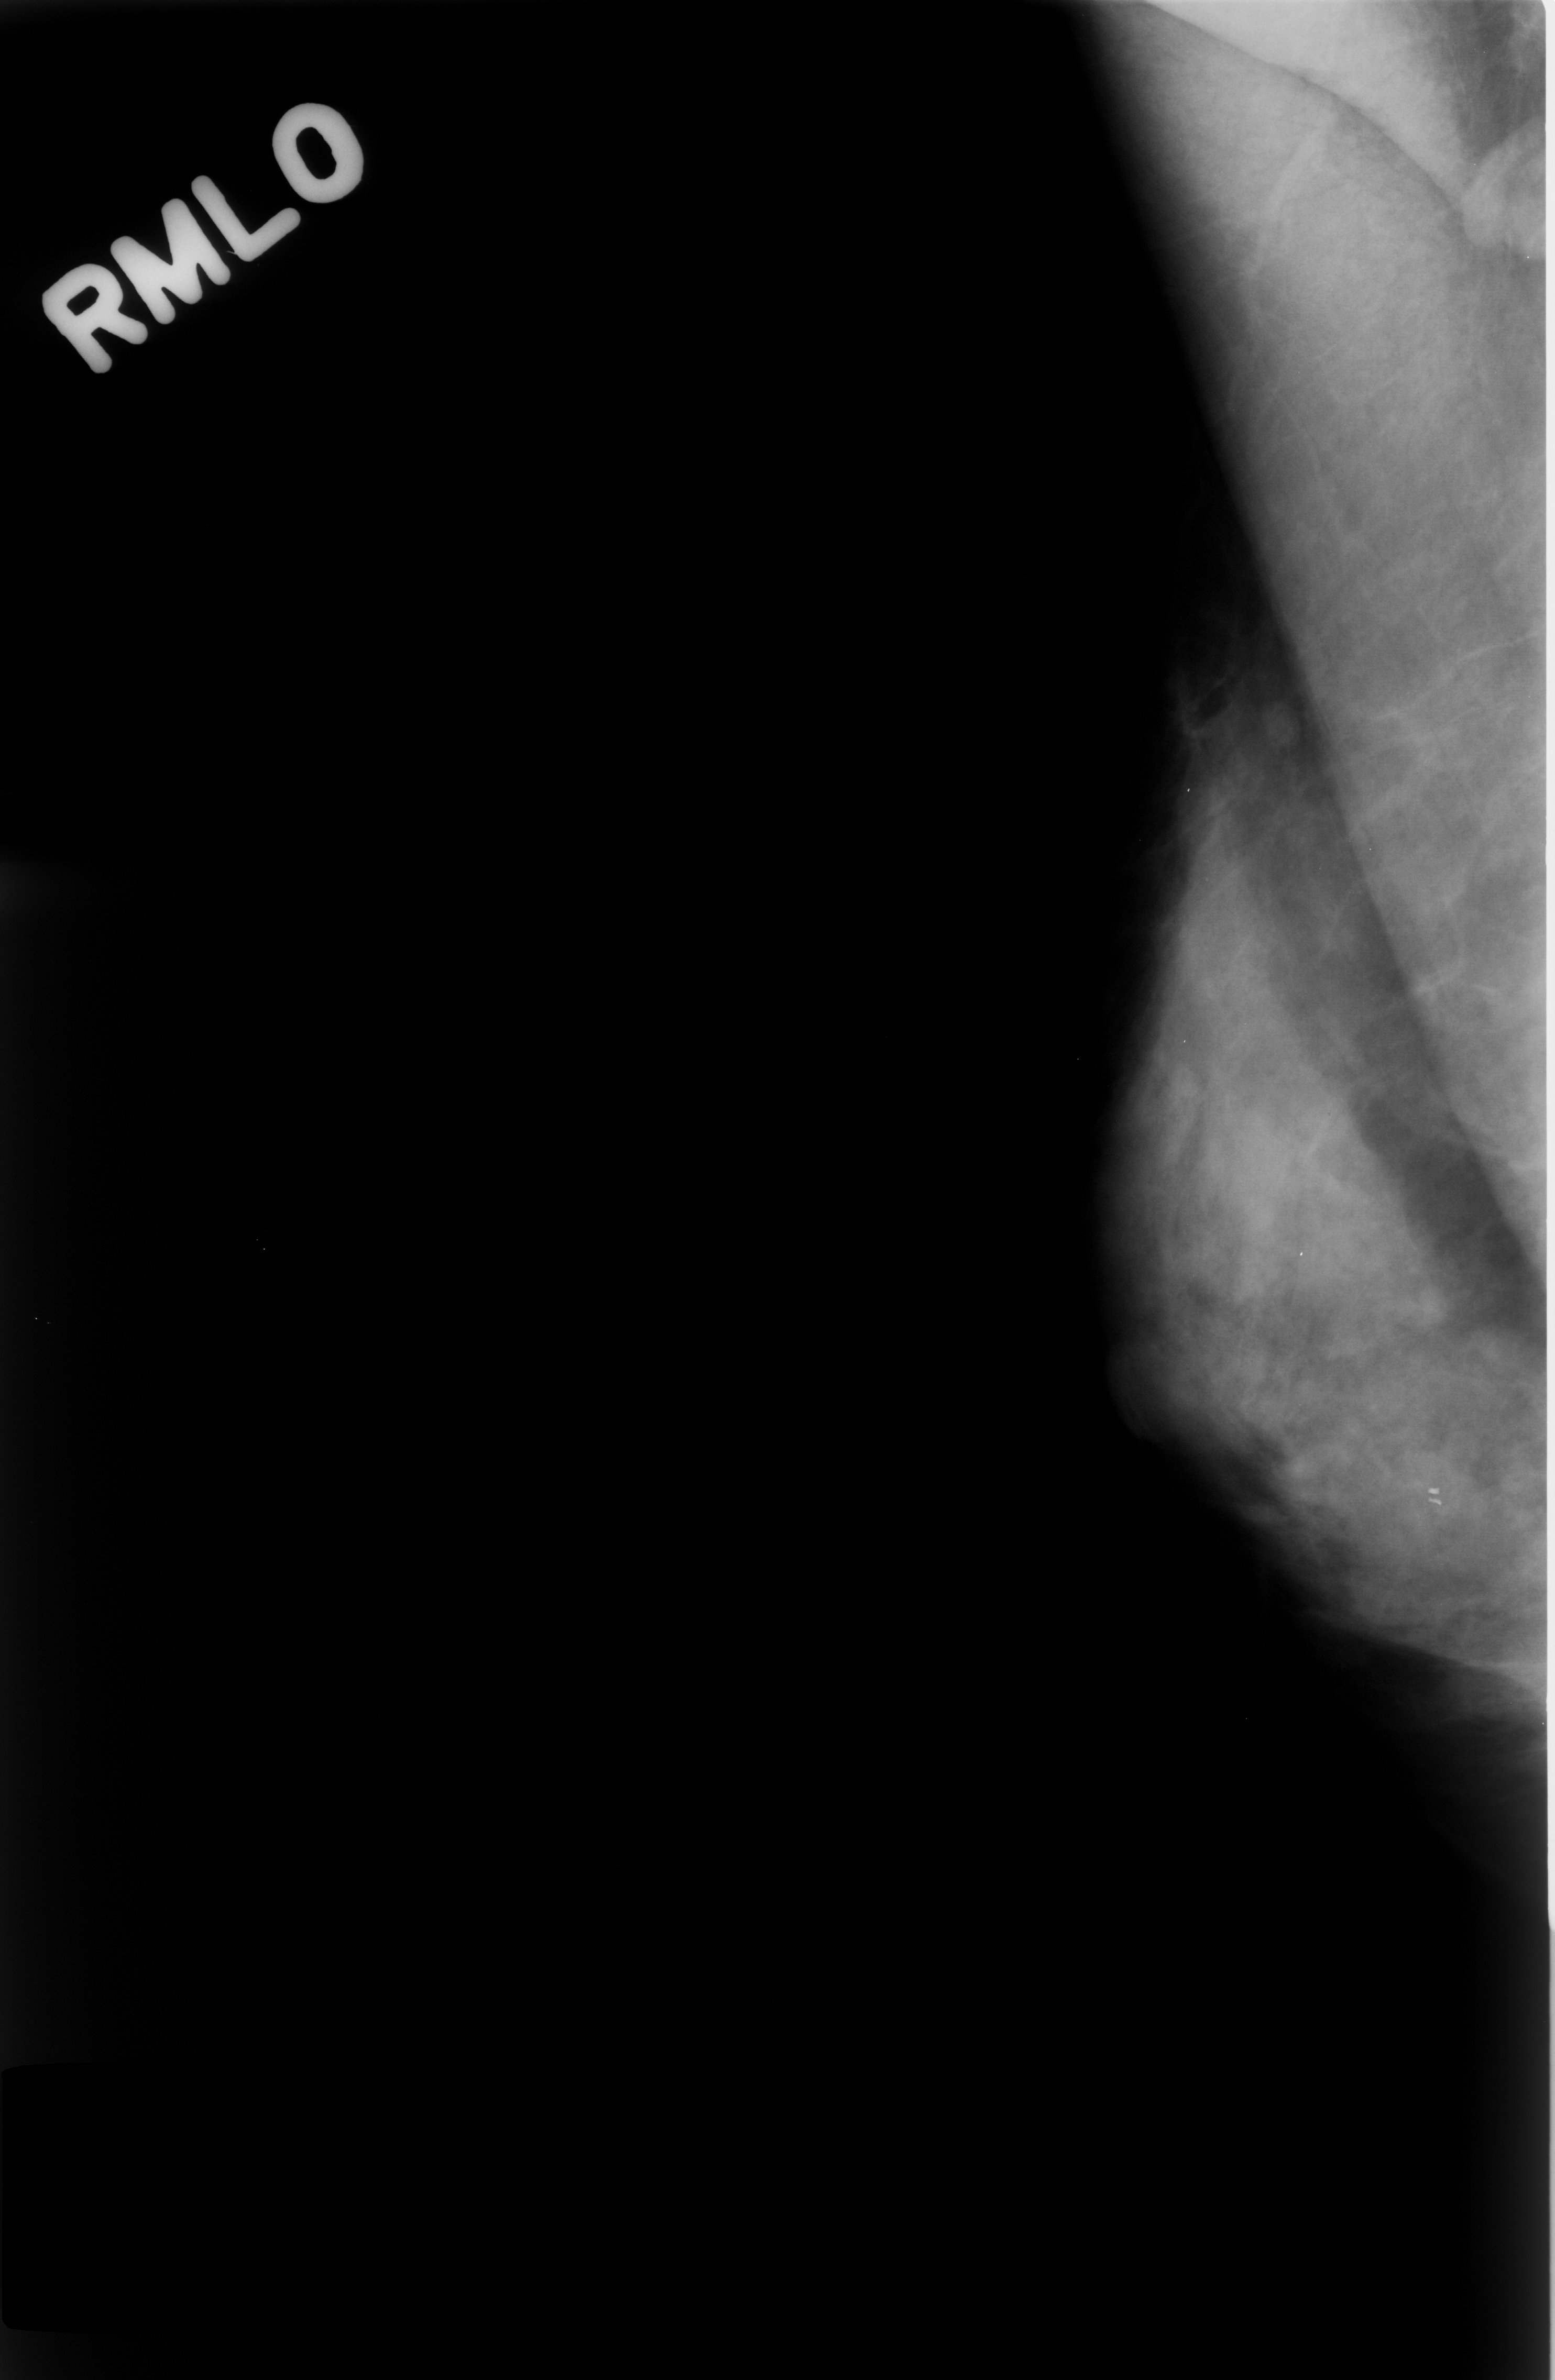
Digitized screen-film mammogram. Right breast. Mediolateral oblique (MLO) view. BI-RADS breast density category 4 (scale 1–4). 1555 × 2380 image matrix.
Expert-marked regions of interest on this film, with their recorded descriptors:
- mass, shape oval, margins circumscribed; BI-RADS assessment category 3; benign; no additional work-up was recommended (outcome (as recorded, no biopsy): benign without callback): bounding box [x1, y1, x2, y2] px = [1249, 664, 1331, 773]